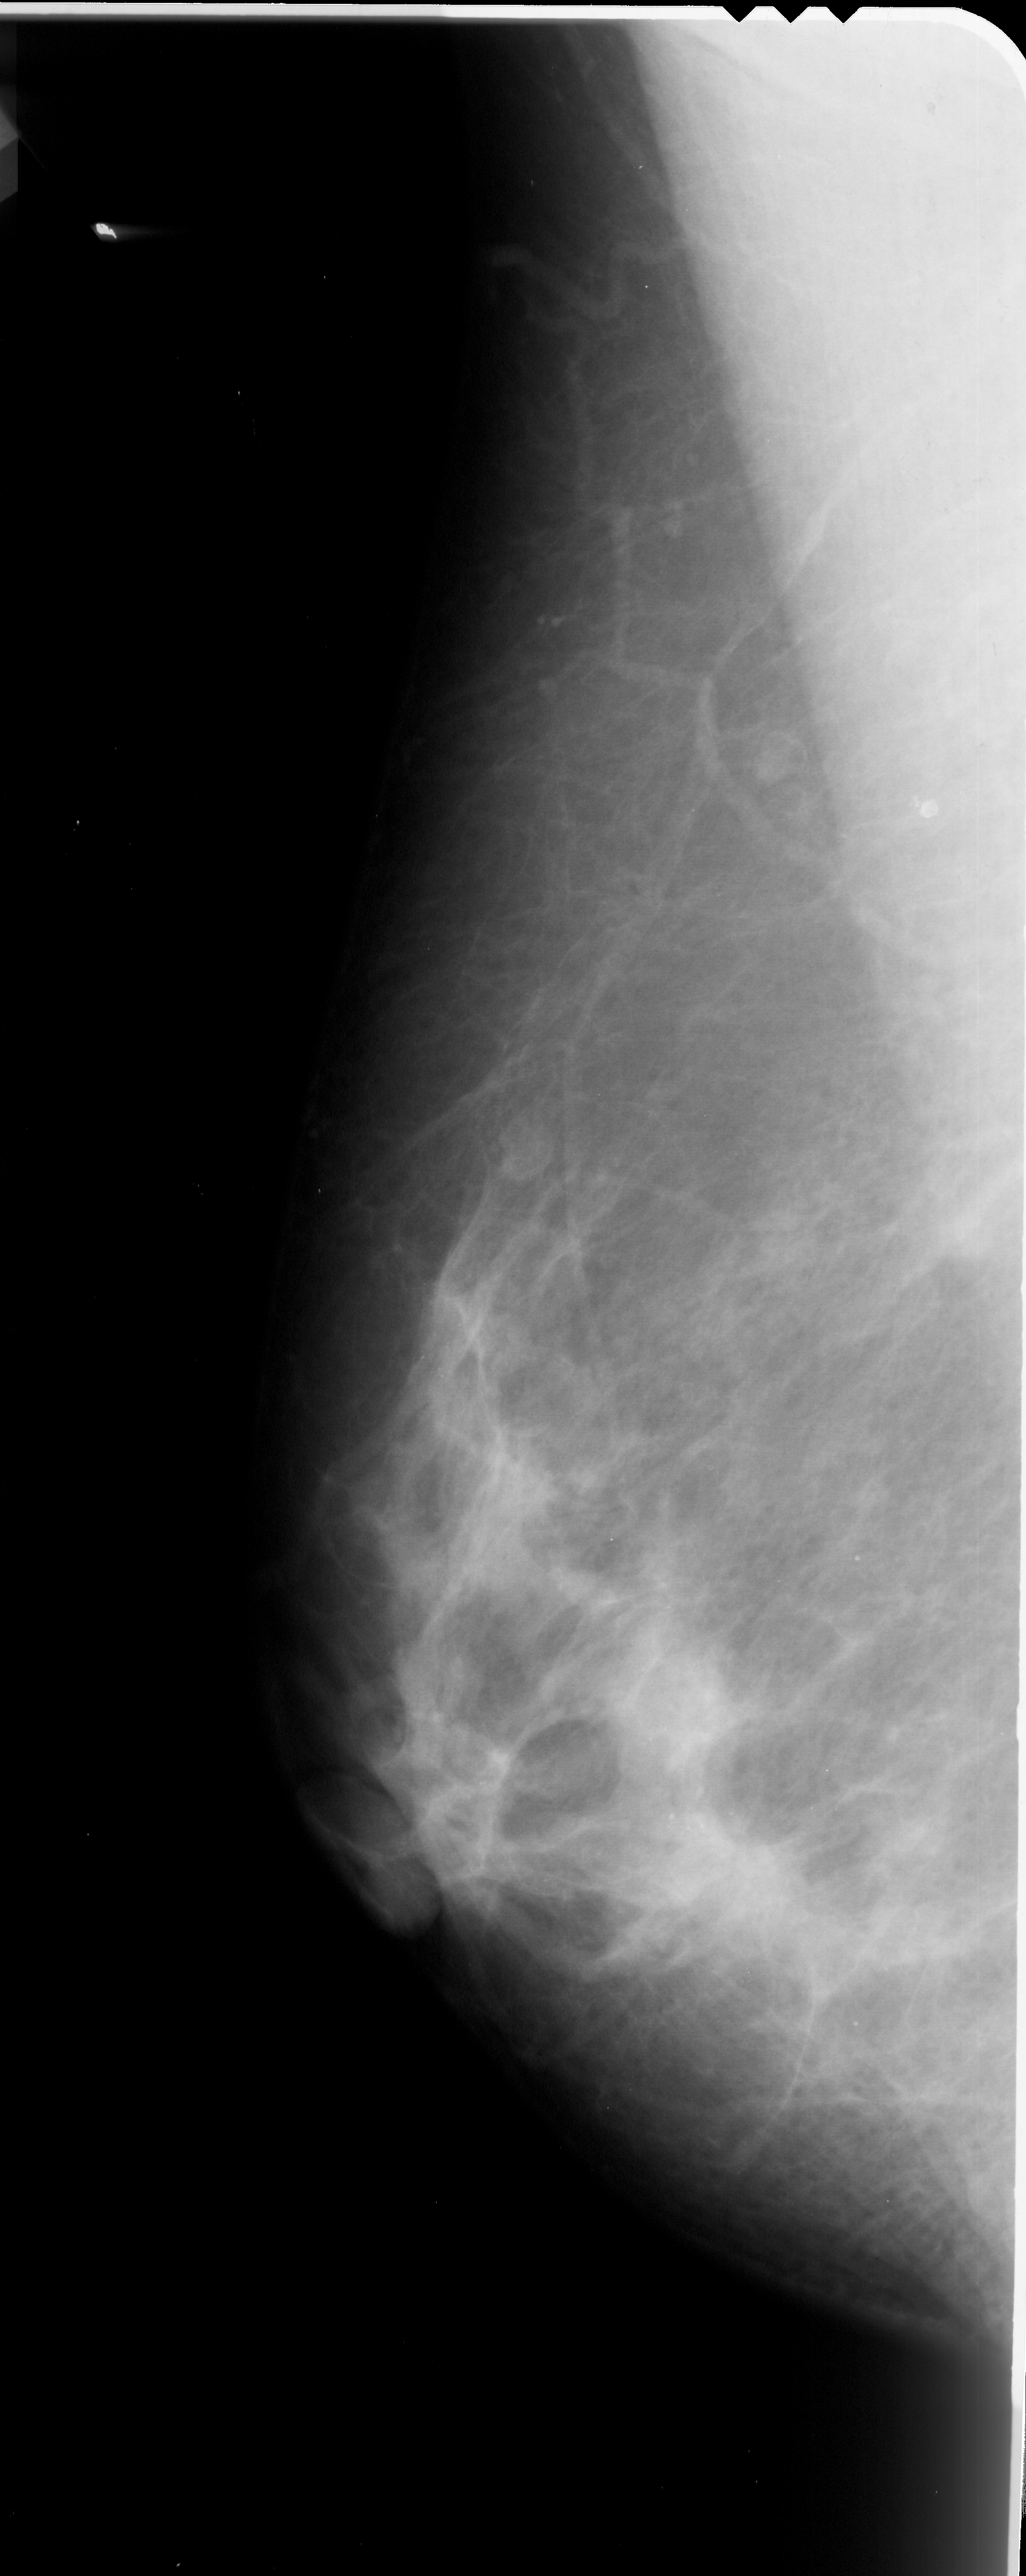
Digitized screen-film mammogram. Left breast. MLO view. BI-RADS breast density category 3 (scale 1–4). 1026 × 2576 image matrix.
Expert-marked regions of interest on this image (one box per marked abnormality):
- calcifications, morphology pleomorphic, distribution clustered; BI-RADS assessment category 4; pathology (as recorded): malignant: bounding box <628,1703,751,1898> (left, top, right, bottom; pixels)